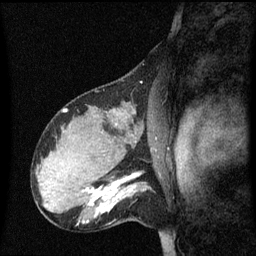
Breast MRI (dynamic contrast-enhanced), one sagittal slice; dynamic contrast-enhanced series, image 2 of 3 at this slice position (ordered by acquisition); 1.5 T; TE 4.2 ms, TR 8.4 ms; 2.1 mm slice thickness; 256 × 256 image matrix, field of view 210 × 210 mm. Patient: female, 31 years. Case-level facts recorded for this patient, not image findings: setting: breast cancer imaged before/during neoadjuvant chemotherapy; receptor status: HR-positive, HER2-negative.
Annotated regions visible in this slice (semi-automatic segmentation, software-assisted and operator-edited):
- analysis volume of interest (the breast-tissue region the enhancement analysis was run in; not a lesion): bounding box [x1, y1, x2, y2] px = [98, 175, 150, 226]
- tumour enhancement mask (voxels above the 70 % enhancement threshold inside the analysis volume of interest): [98, 175, 140, 213]